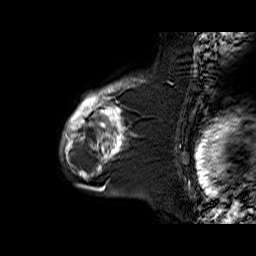
Breast MRI (dynamic contrast-enhanced), one sagittal slice. Slice 49 of 60 in the series (ordered by position). Dynamic contrast-enhanced series, time point 2 of 6 at this slice position (early post-contrast). 1.5 T. TE 6.3 ms, TR 32.9 ms. 256 × 256 image matrix, field of view 200 × 200 mm. Female patient. From the clinical record (not read from this slice): setting: breast cancer imaged before/during neoadjuvant chemotherapy; receptor status: triple-negative.
Outlined on this slice (semi-automatic segmentation, software-assisted and operator-edited):
- analysis volume of interest (the breast-tissue region the enhancement analysis was run in; not a lesion): box from (x=60, y=81) to (x=145, y=170) px
- tumour enhancement mask (voxels above the 100 % enhancement threshold inside the analysis volume of interest): (x=61, y=81)–(x=128, y=170)